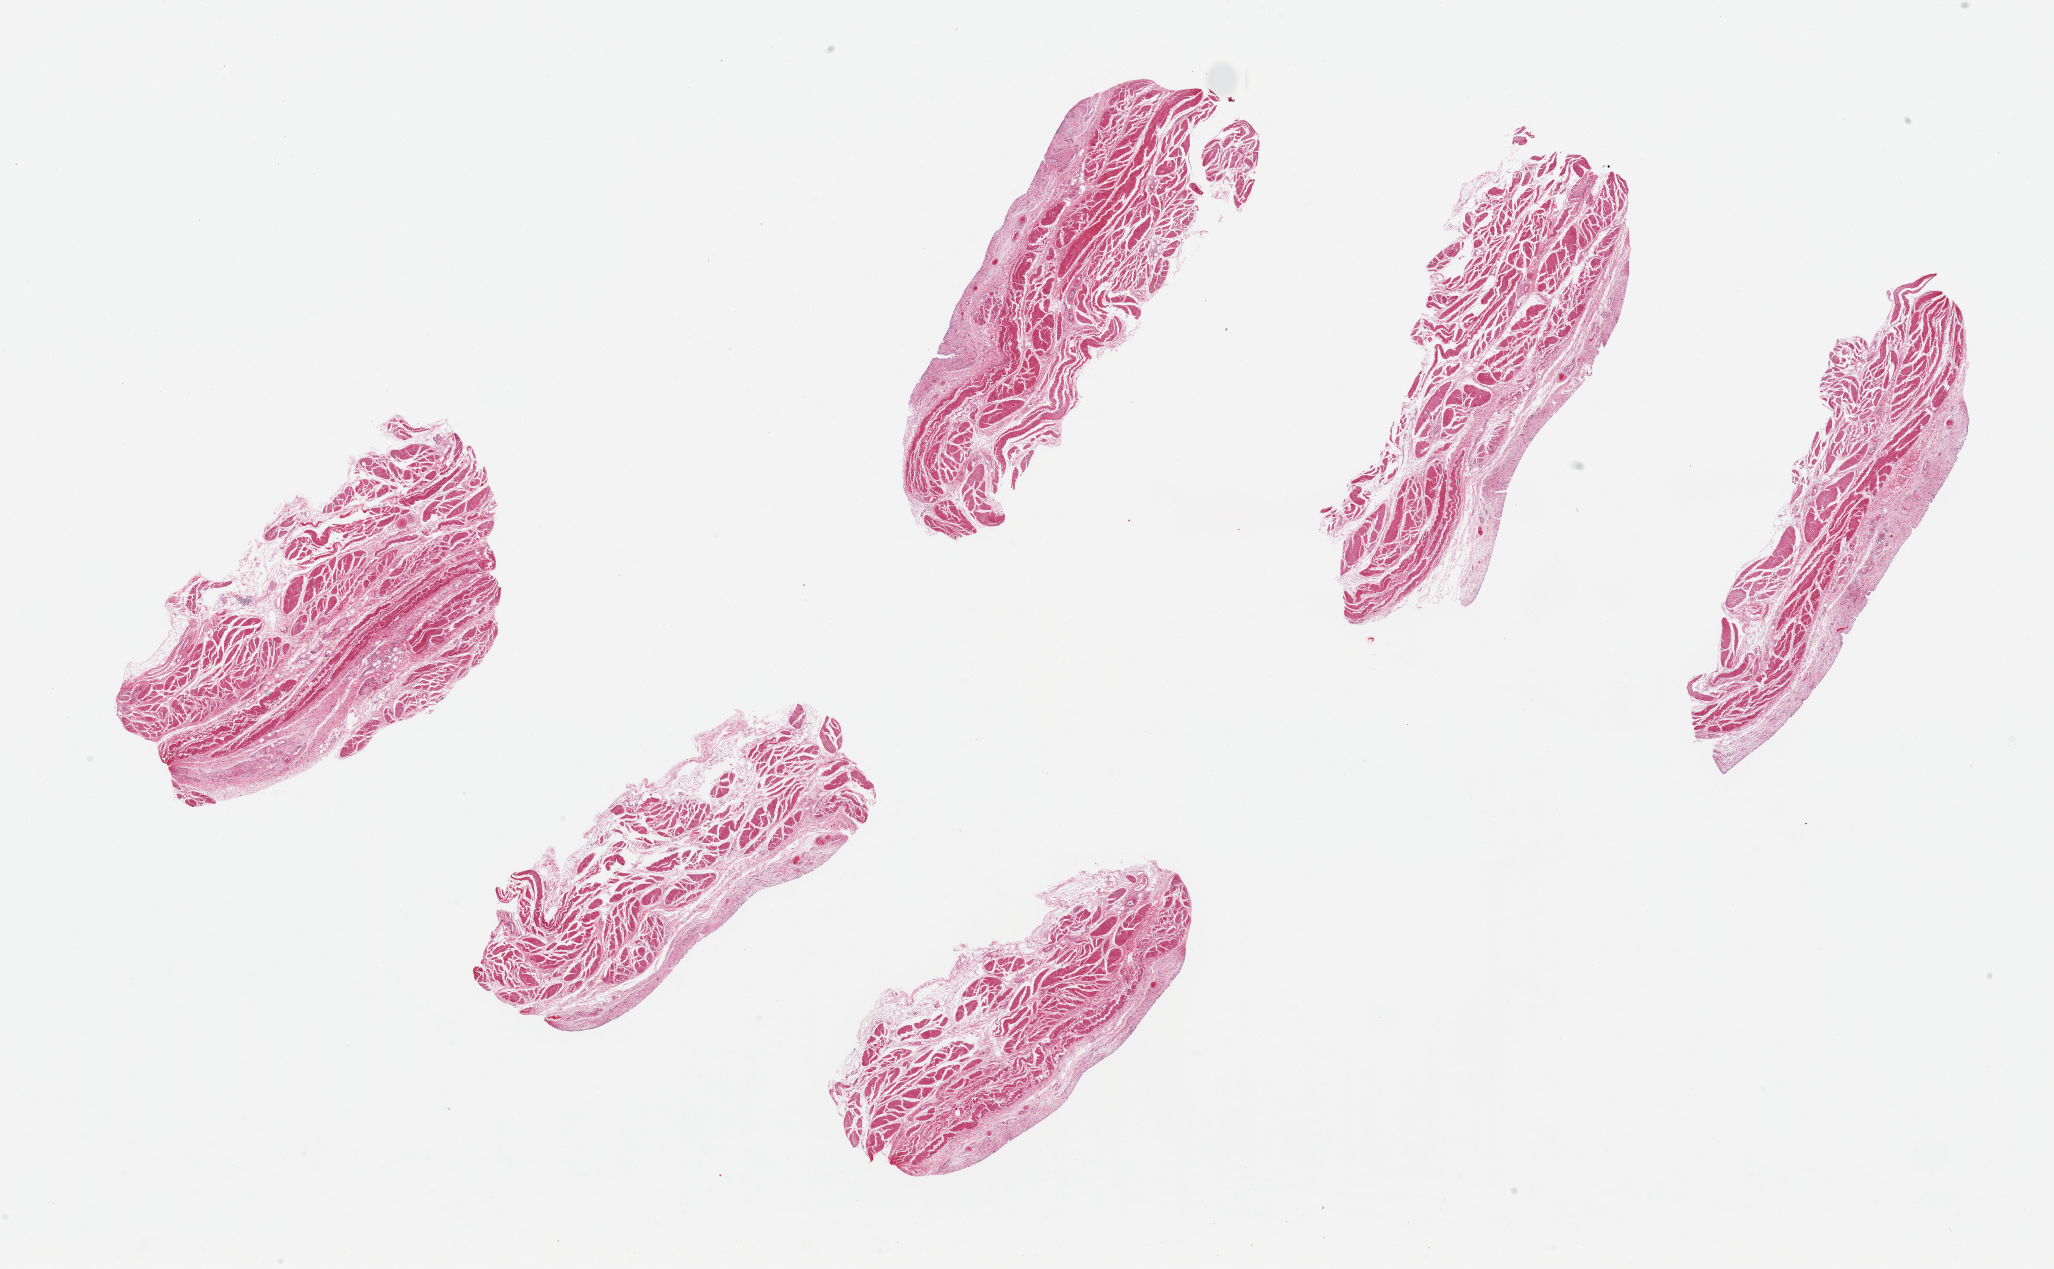
Whole-slide image, hematoxylin and eosin (H&E) stain, a low-resolution overview of the entire scanned area, about 32.5 x 20.1 mm (from a 20x scan), PAXgene-fixed paraffin-embedded (PFPE) section, section of urinary bladder (target tissue), tissue donor sample. Donor: male.
- review note (as recorded): 6 pieces up to 8x3.4 mm; epithelium totally sloughed on all; muscle slightly autolyzed